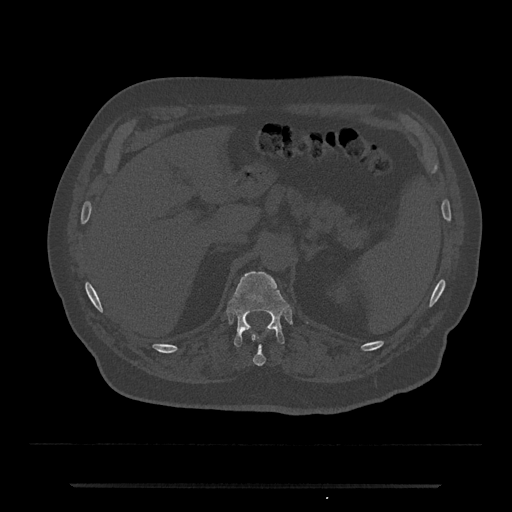
CT including the spine, one axial slice; reconstruction kernel Br40s/3; 120 kVp; bone window (W 1800 / L 400 HU); 512 × 512 image matrix. Patient: male, 80 years. From the clinical record (not read from this slice): primary cancer: prostate; vertebrae with lytic lesions (as recorded): L1, T11.
Outlined on this slice (semi-automatic segmentation, software-assisted and operator-edited):
- T11 vertebra: bounding box <253,335,266,366> (left, top, right, bottom; pixels)
- T12 vertebra: <228,271,289,347>